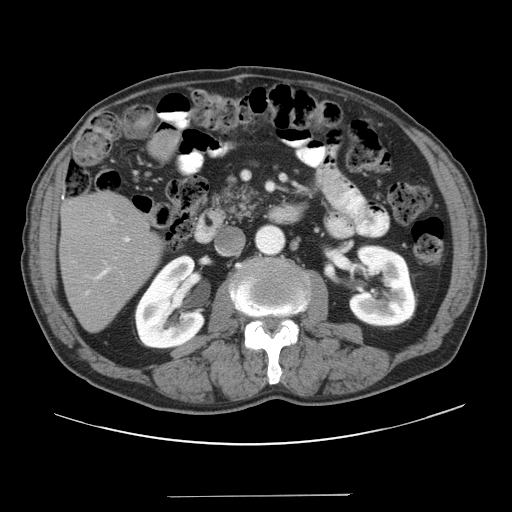
Contrast-enhanced abdominal CT, one axial slice; slice 11 of 41 in the series (ordered by position); 120 kVp; intravenous contrast given; soft-tissue window (W 400 / L 40 HU); 5 mm slice thickness; 512 × 512 image matrix, field of view 420 × 420 mm. Male patient, age 75 years. Case-level facts recorded for this patient, not image findings: diagnosis: colorectal cancer liver metastases, imaged before liver resection; multiple liver metastases: no; largest metastasis: 5.2 cm.
Annotated regions visible in this slice (expert manual segmentation):
- liver: bounding box <60,194,162,331> (left, top, right, bottom; pixels)
- planned liver remnant (the part of the liver to remain after resection): <60,194,162,331>
- portal vein (with intrahepatic branches): <85,212,131,295>